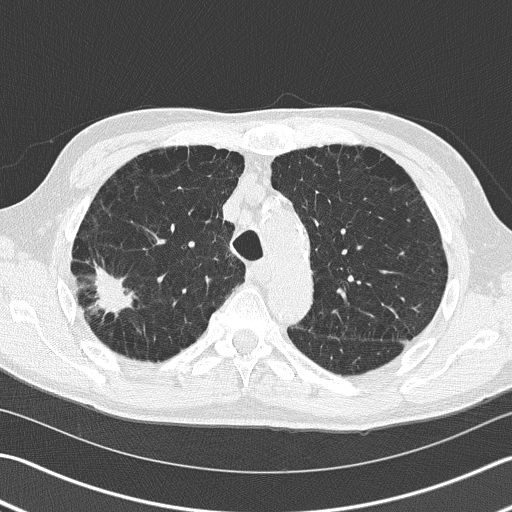
Low-dose screening chest CT, one axial slice; position 115 of 163 along the scan axis; reconstruction kernel B50f; lung window (W 1500 / L -600 HU); 2 mm slice thickness; 512 × 512 image matrix.
Structures marked on this image (manually delineated by an expert):
- lesion 1 (tumor, upper lobe of right lung): bounding box <94,263,134,315> (left, top, right, bottom; pixels)